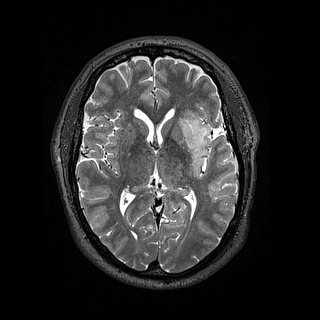
Brain MRI from a brain-tumour surgery series, one axial slice. 320 × 320 image matrix, field of view 254 × 254 mm. Case-level facts recorded for this patient, not image findings: histopathology: Astrocytoma; WHO grade: 2.
Structures marked on this image (manually delineated by an expert):
- tumour: box from (x=180, y=110) to (x=211, y=177) px